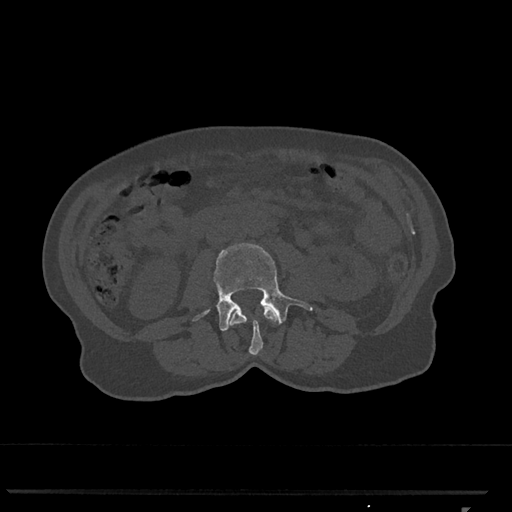
CT including the spine, one axial slice; position 293 of 793 along the scan axis; reconstruction kernel Br40s/3; bone window (W 1800 / L 400 HU); 0.5 mm slice thickness; 512 × 512 image matrix, field of view 380 × 380 mm. Female patient, age 62 years. From the clinical record (not read from this slice): primary cancer: renal.
Structures marked on this image (semi-automatic segmentation, software-assisted and operator-edited):
- L2 vertebra: box from (x=229, y=306) to (x=278, y=355) px
- L3 vertebra: (x=193, y=243)–(x=313, y=331)